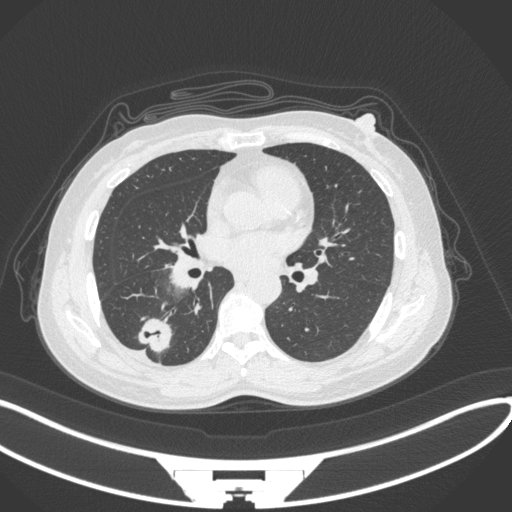
Chest CT, one axial slice; position 148 of 352 along the scan axis; lung window (W 1500 / L -600 HU); 1 mm slice thickness; 512 × 512 image matrix, field of view 400 × 400 mm. Patient: female, 55 years. From the clinical record (not read from this slice): clinical TNM (as recorded): T1c N1 M0.
Structures marked on this image (rectangle marked by the reading radiologist):
- lung tumour (recorded histology: adenocarcinoma): bounding box <135,314,175,357> (left, top, right, bottom; pixels)